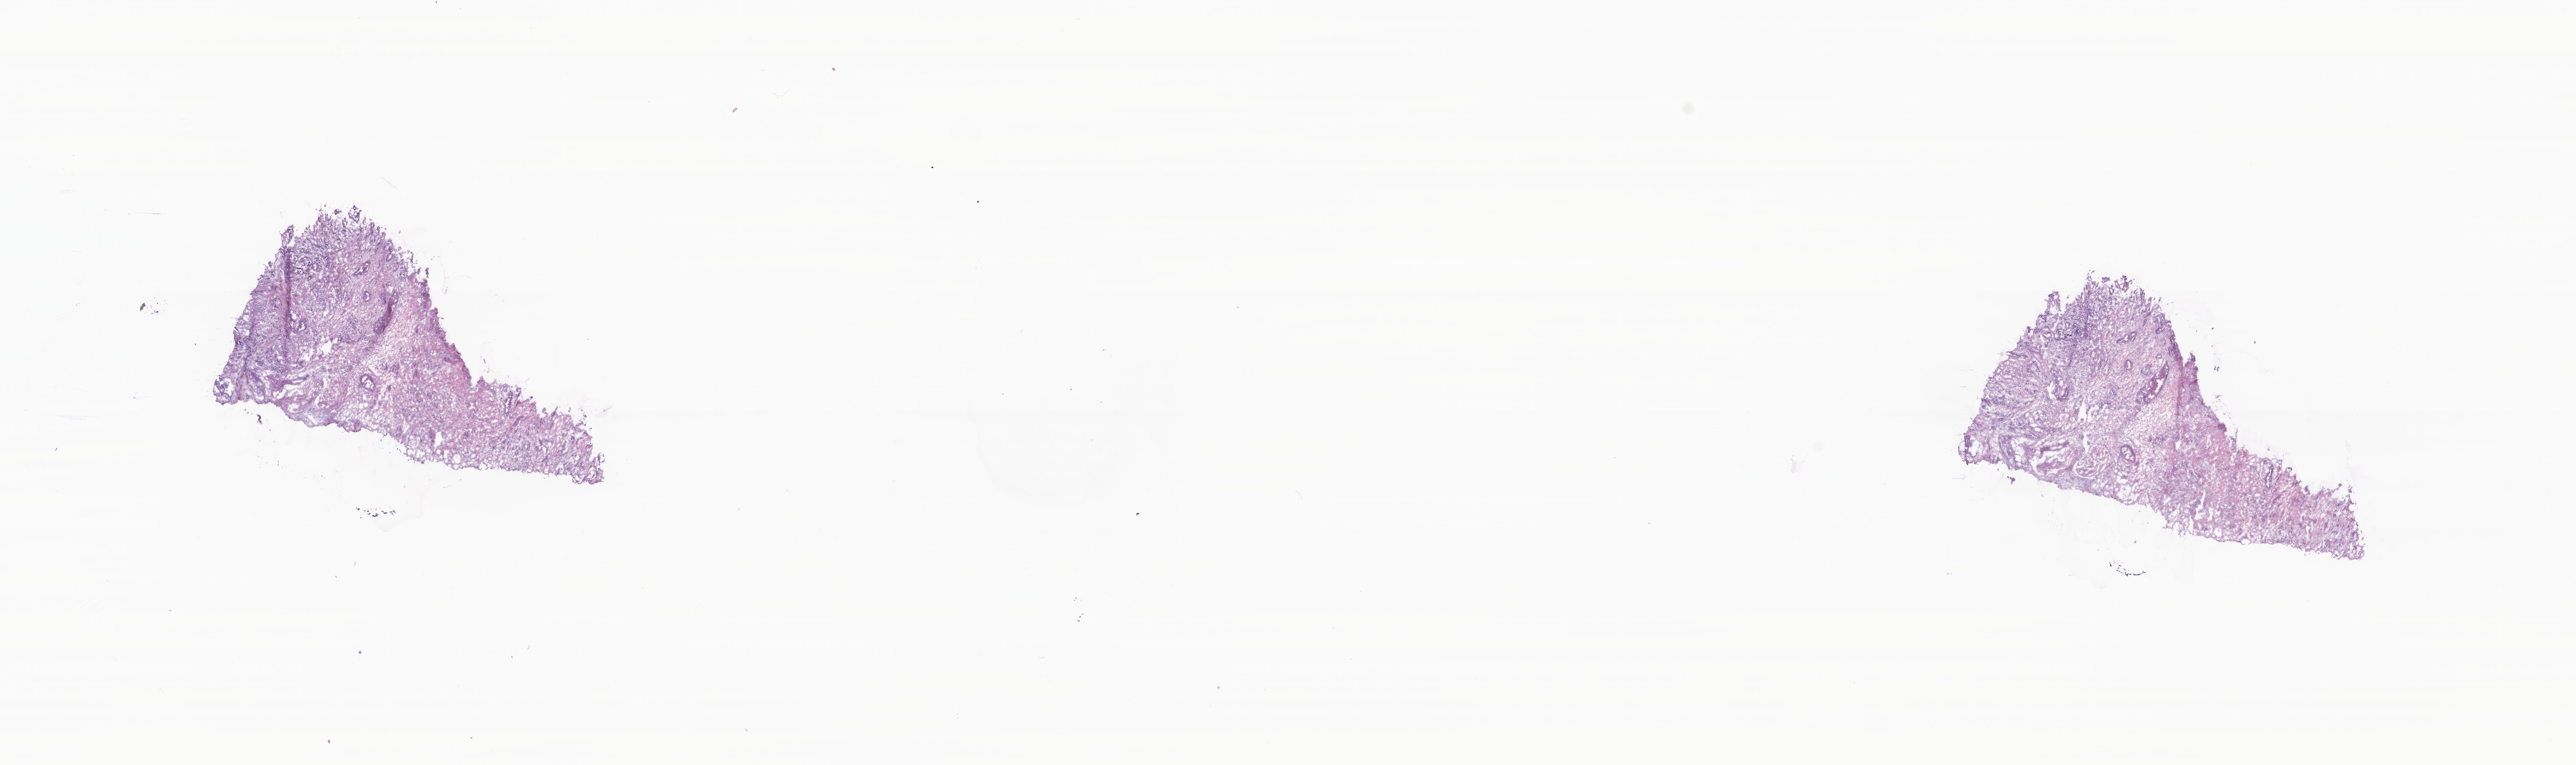
Whole-slide image, H&E stain, a low-resolution overview of the entire scanned area, about 23.1 x 6.9 mm; cryosection; primary tumor; anatomic site: breast. Female patient; age at initial diagnosis 58 years. Composition of this section per pathologist review: tumor cells 100%, tumor nuclei 50%.
Histologic diagnosis: Infiltrating duct carcinoma, NOS.